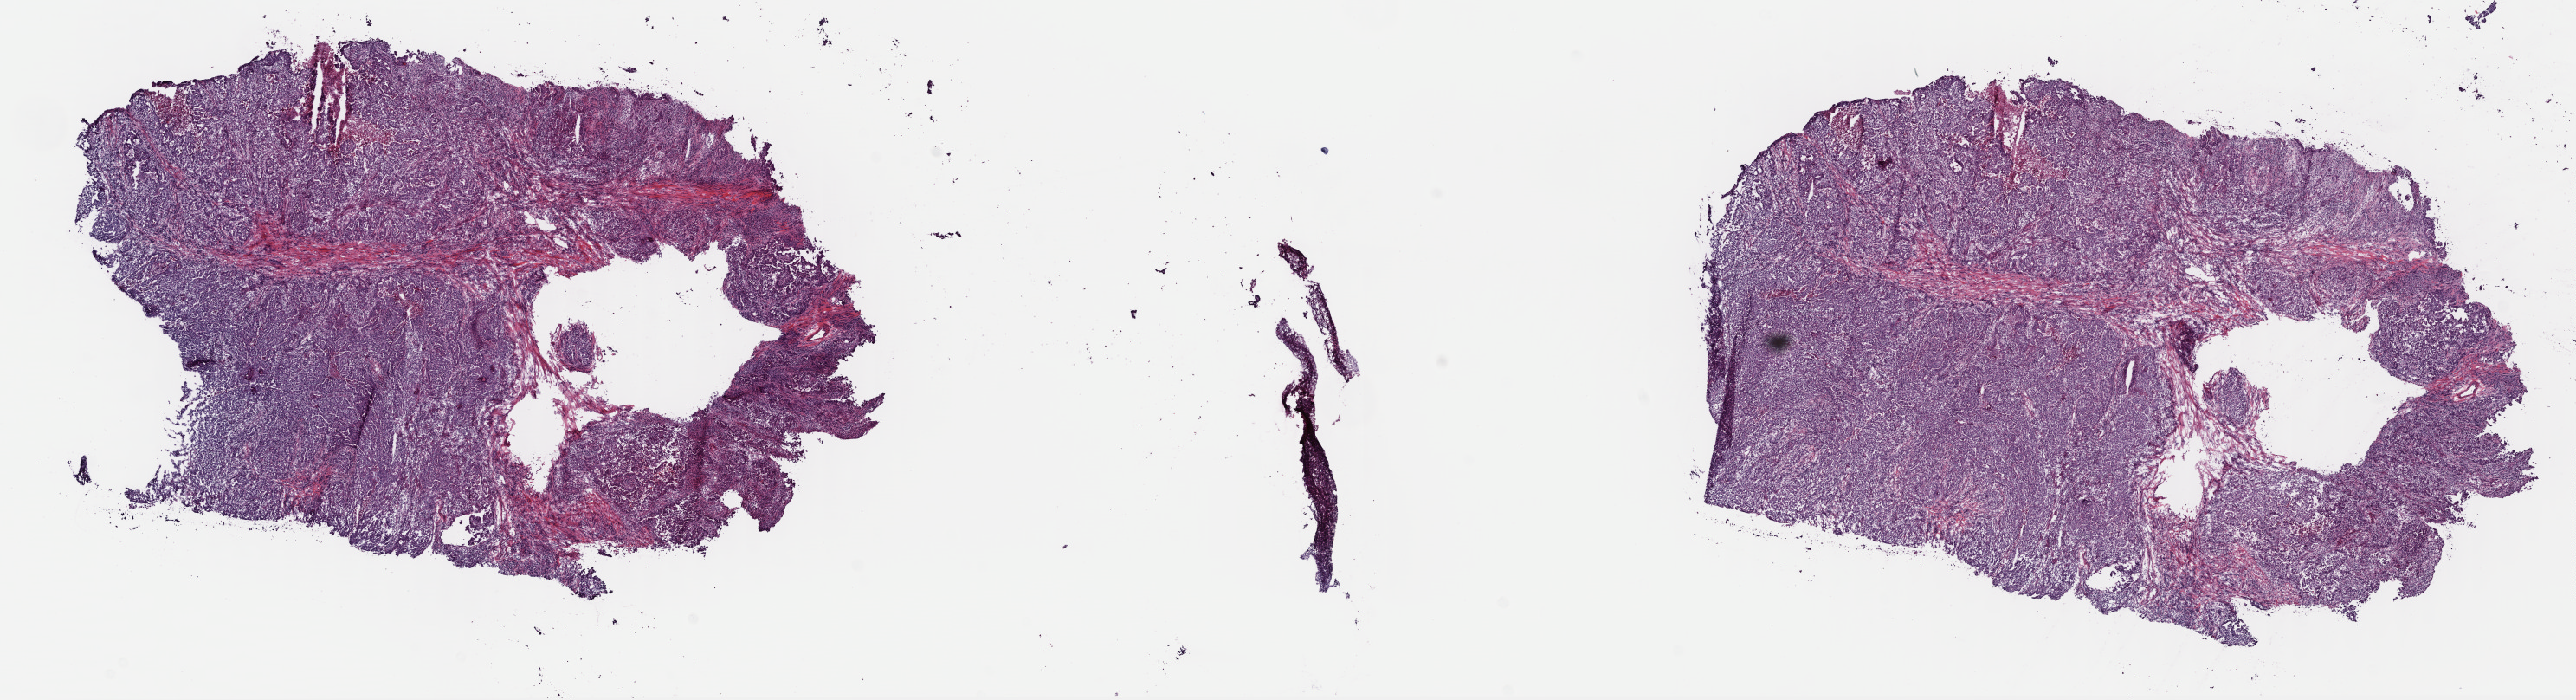
H&E whole-slide image, shown as a low-resolution overview of the whole scanned area (about 23.4 x 6.4 mm, slide scanned at 40x); frozen section from the top of the tissue portion; stomach, primary tumour sample. Male, age 63 years at initial diagnosis. Histologic grade: G3 (poorly differentiated). Pathologist review of this section (percent, as recorded): tumour cells 60%, tumour nuclei 65%, normal cells 0%, stromal cells 28%, necrosis 12%. Inflammatory infiltration, as recorded: lymphocyte infiltration 20%, monocyte infiltration 2%, neutrophil infiltration 10%.
AJCC pathologic stage: IIB (7th edition). Lymph nodes positive (case pathology): 1 of 19 examined. Pathologic diagnosis: Adenocarcinoma, NOS (fundus of stomach). TNM: T3 N1 M0.